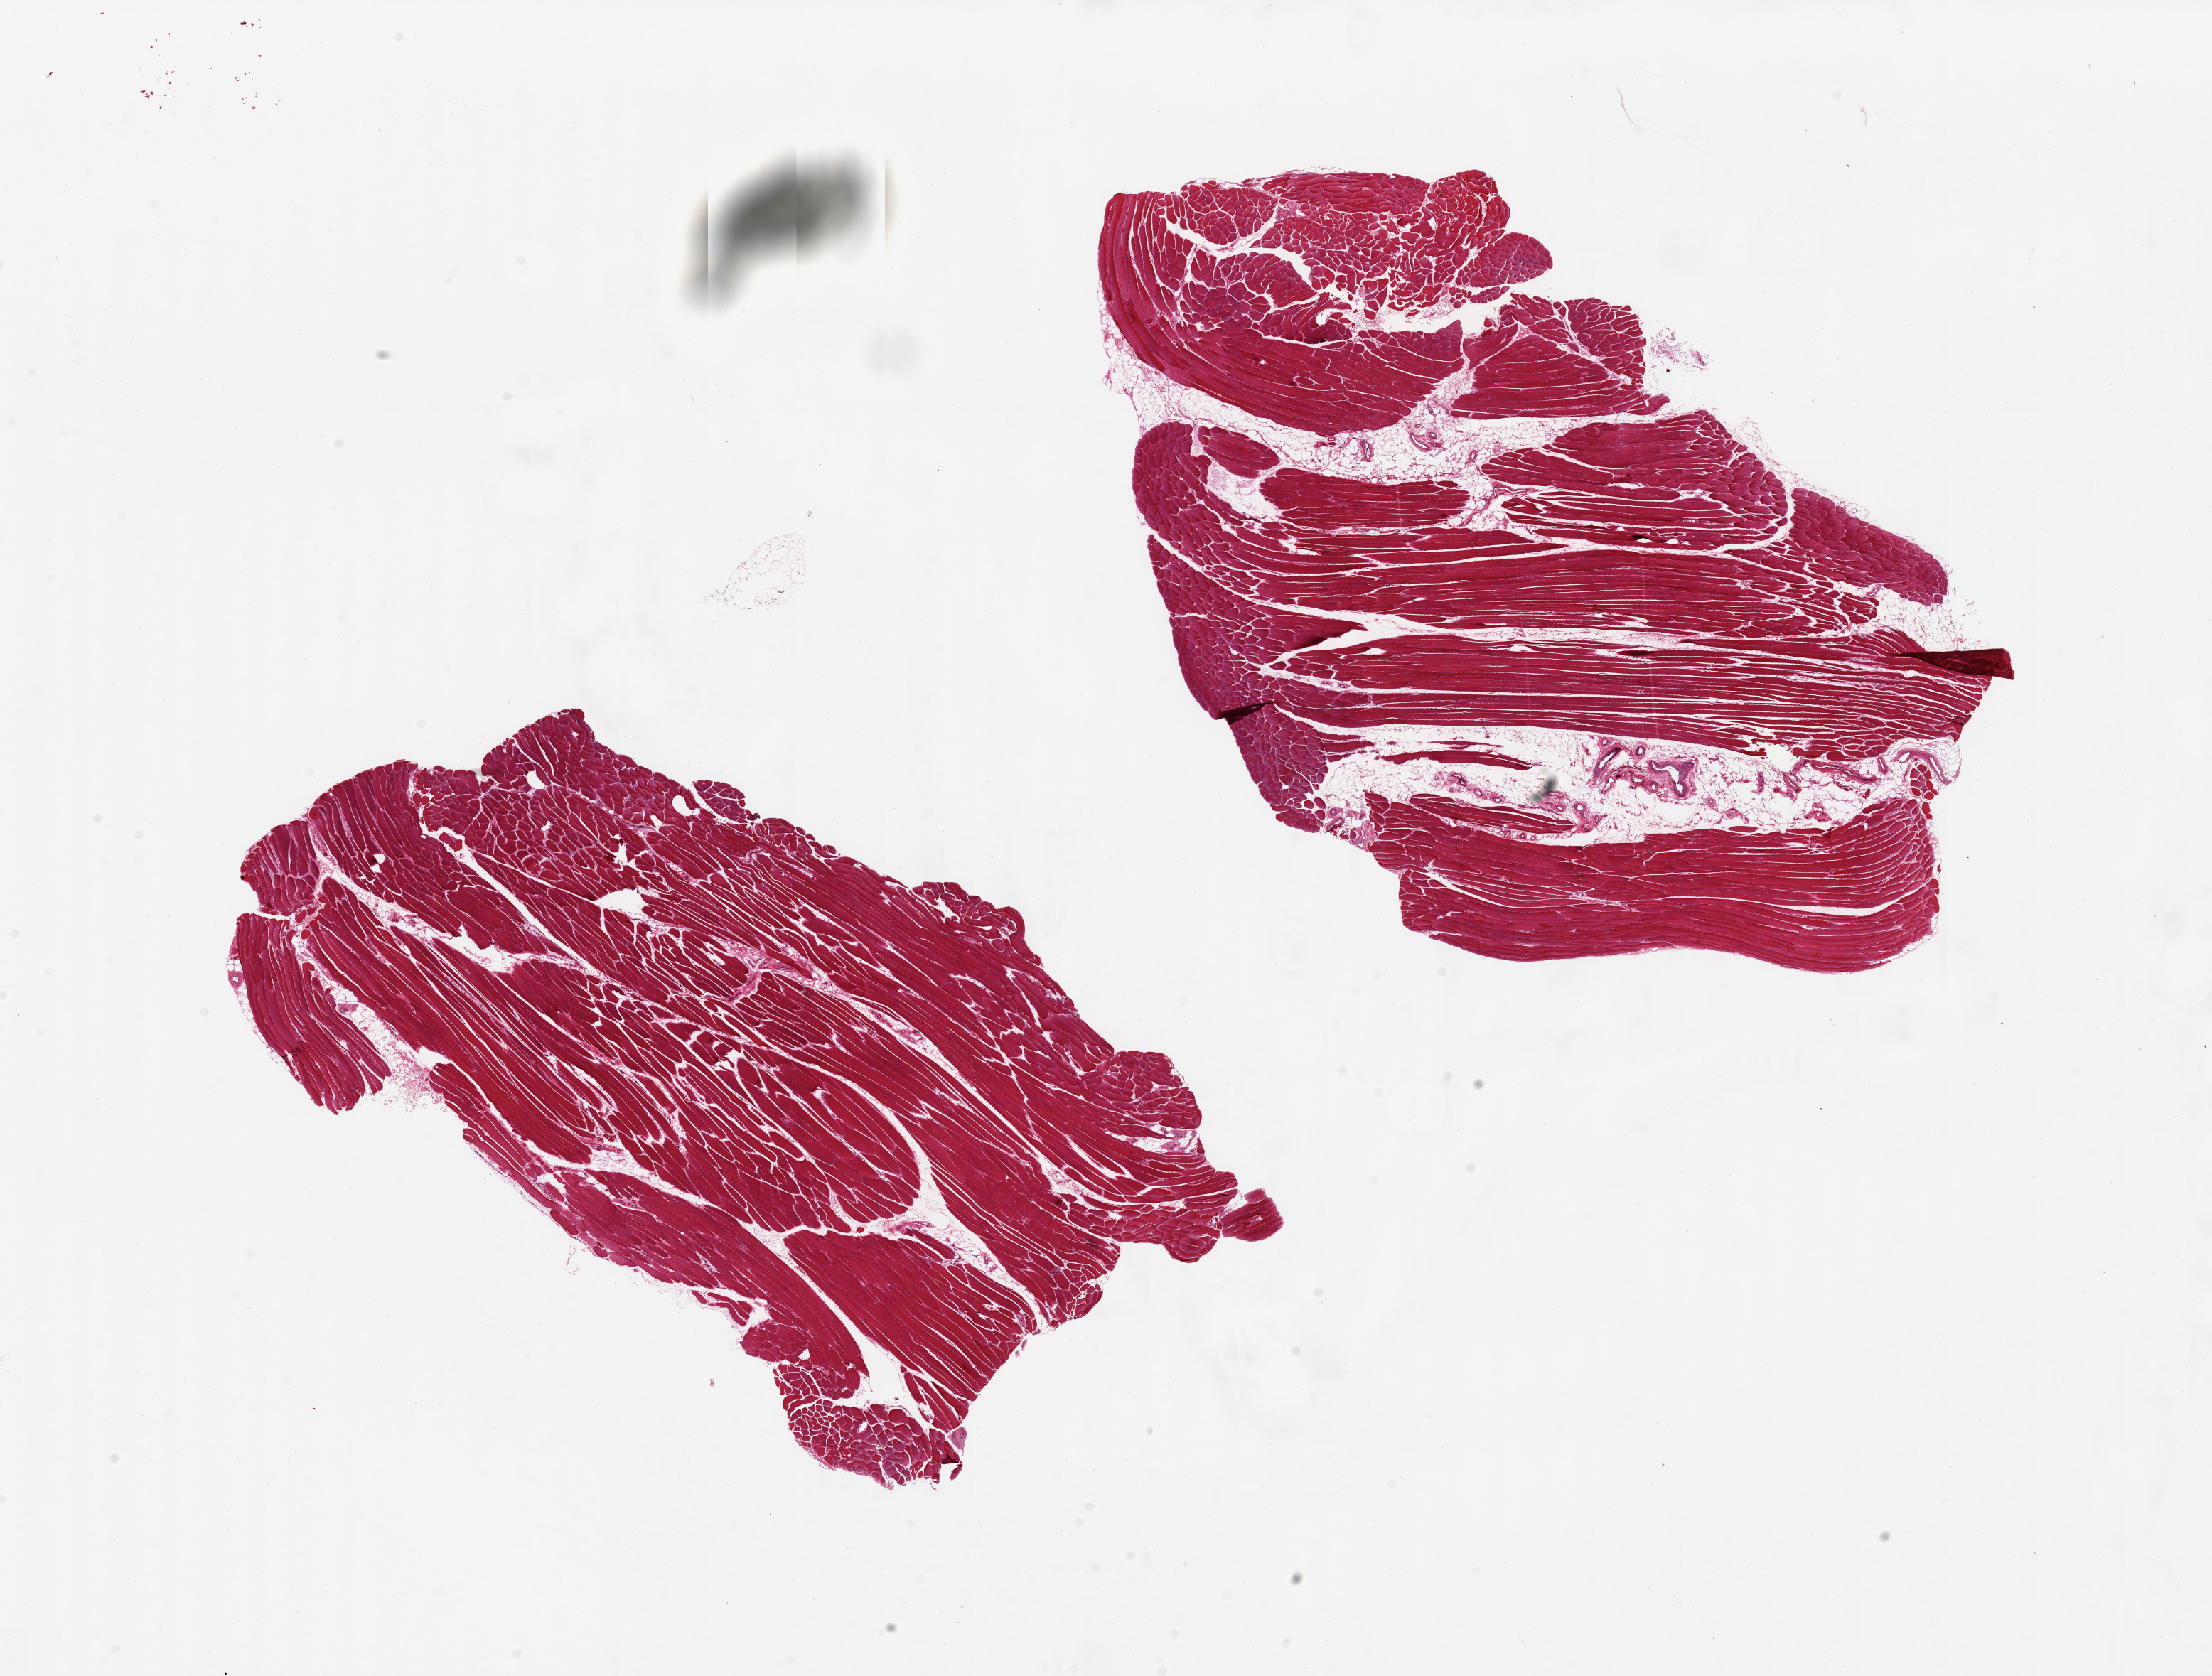
Haematoxylin and eosin whole-slide image — a low-resolution overview of the entire scanned area, about 24.6 x 18.6 mm (slide scanned at 20x), PAXgene-fixed paraffin-embedded (PFPE) section, section of skeletal muscle (target tissue), donor tissue sample. Donor: male.
Reviewer comment on this tissue sample: 2 pieces, 11x7 & 10x9mm; ~10% interstital fat.